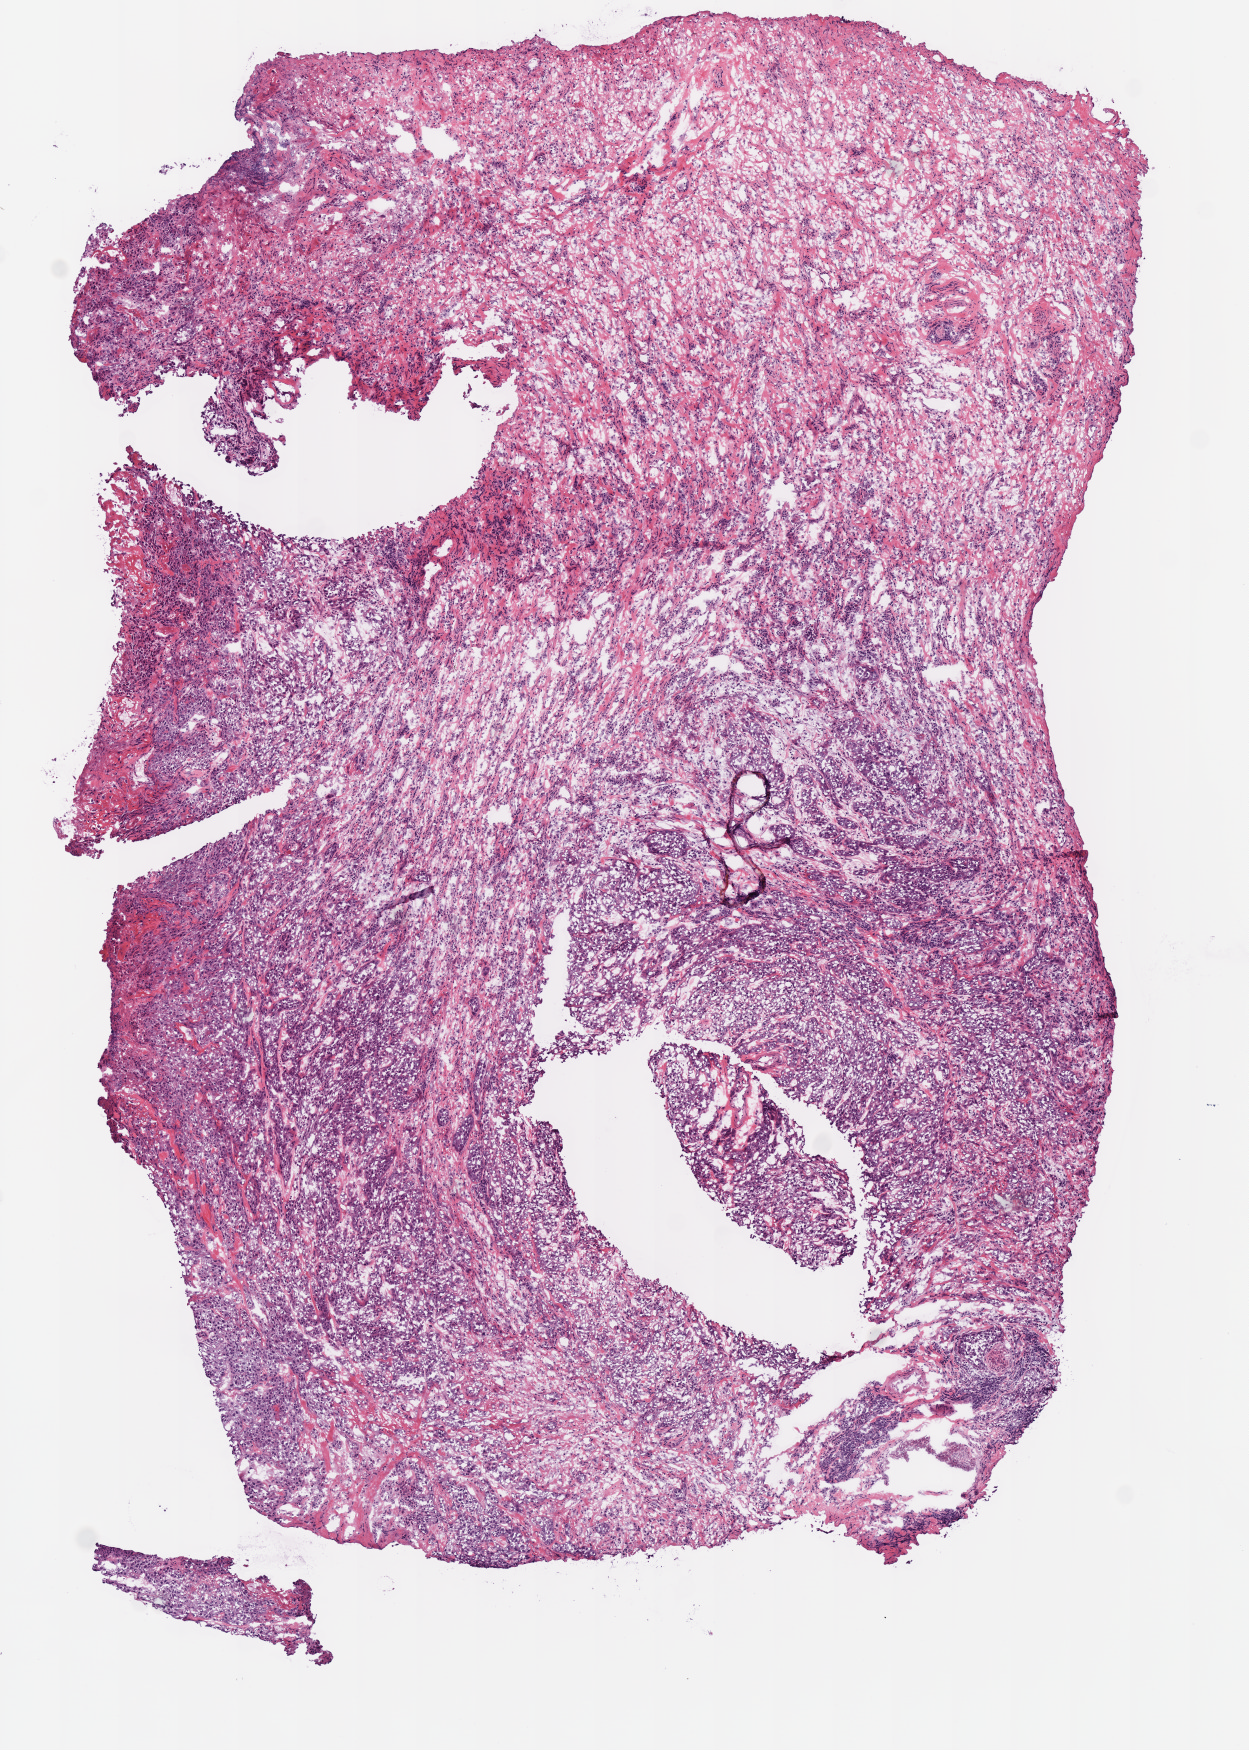
H&E-stained whole-slide image, shown as a low-resolution overview of the whole scanned area (about 4.9 x 6.9 mm, from a 40x scan). Frozen section from the top of the tissue portion. Primary tumour sample from the head and neck. Male patient; age at initial diagnosis 38 years. Histologic grade: GX (grade cannot be assessed). Pathologist review of this section (percent, as recorded): tumour cells 50%, tumour nuclei 60%, normal cells 0%, stromal cells 50%, necrosis 0%.
* pathologic diagnosis: Squamous cell carcinoma, NOS (larynx, NOS)
* AJCC pathologic stage: II (7th edition)